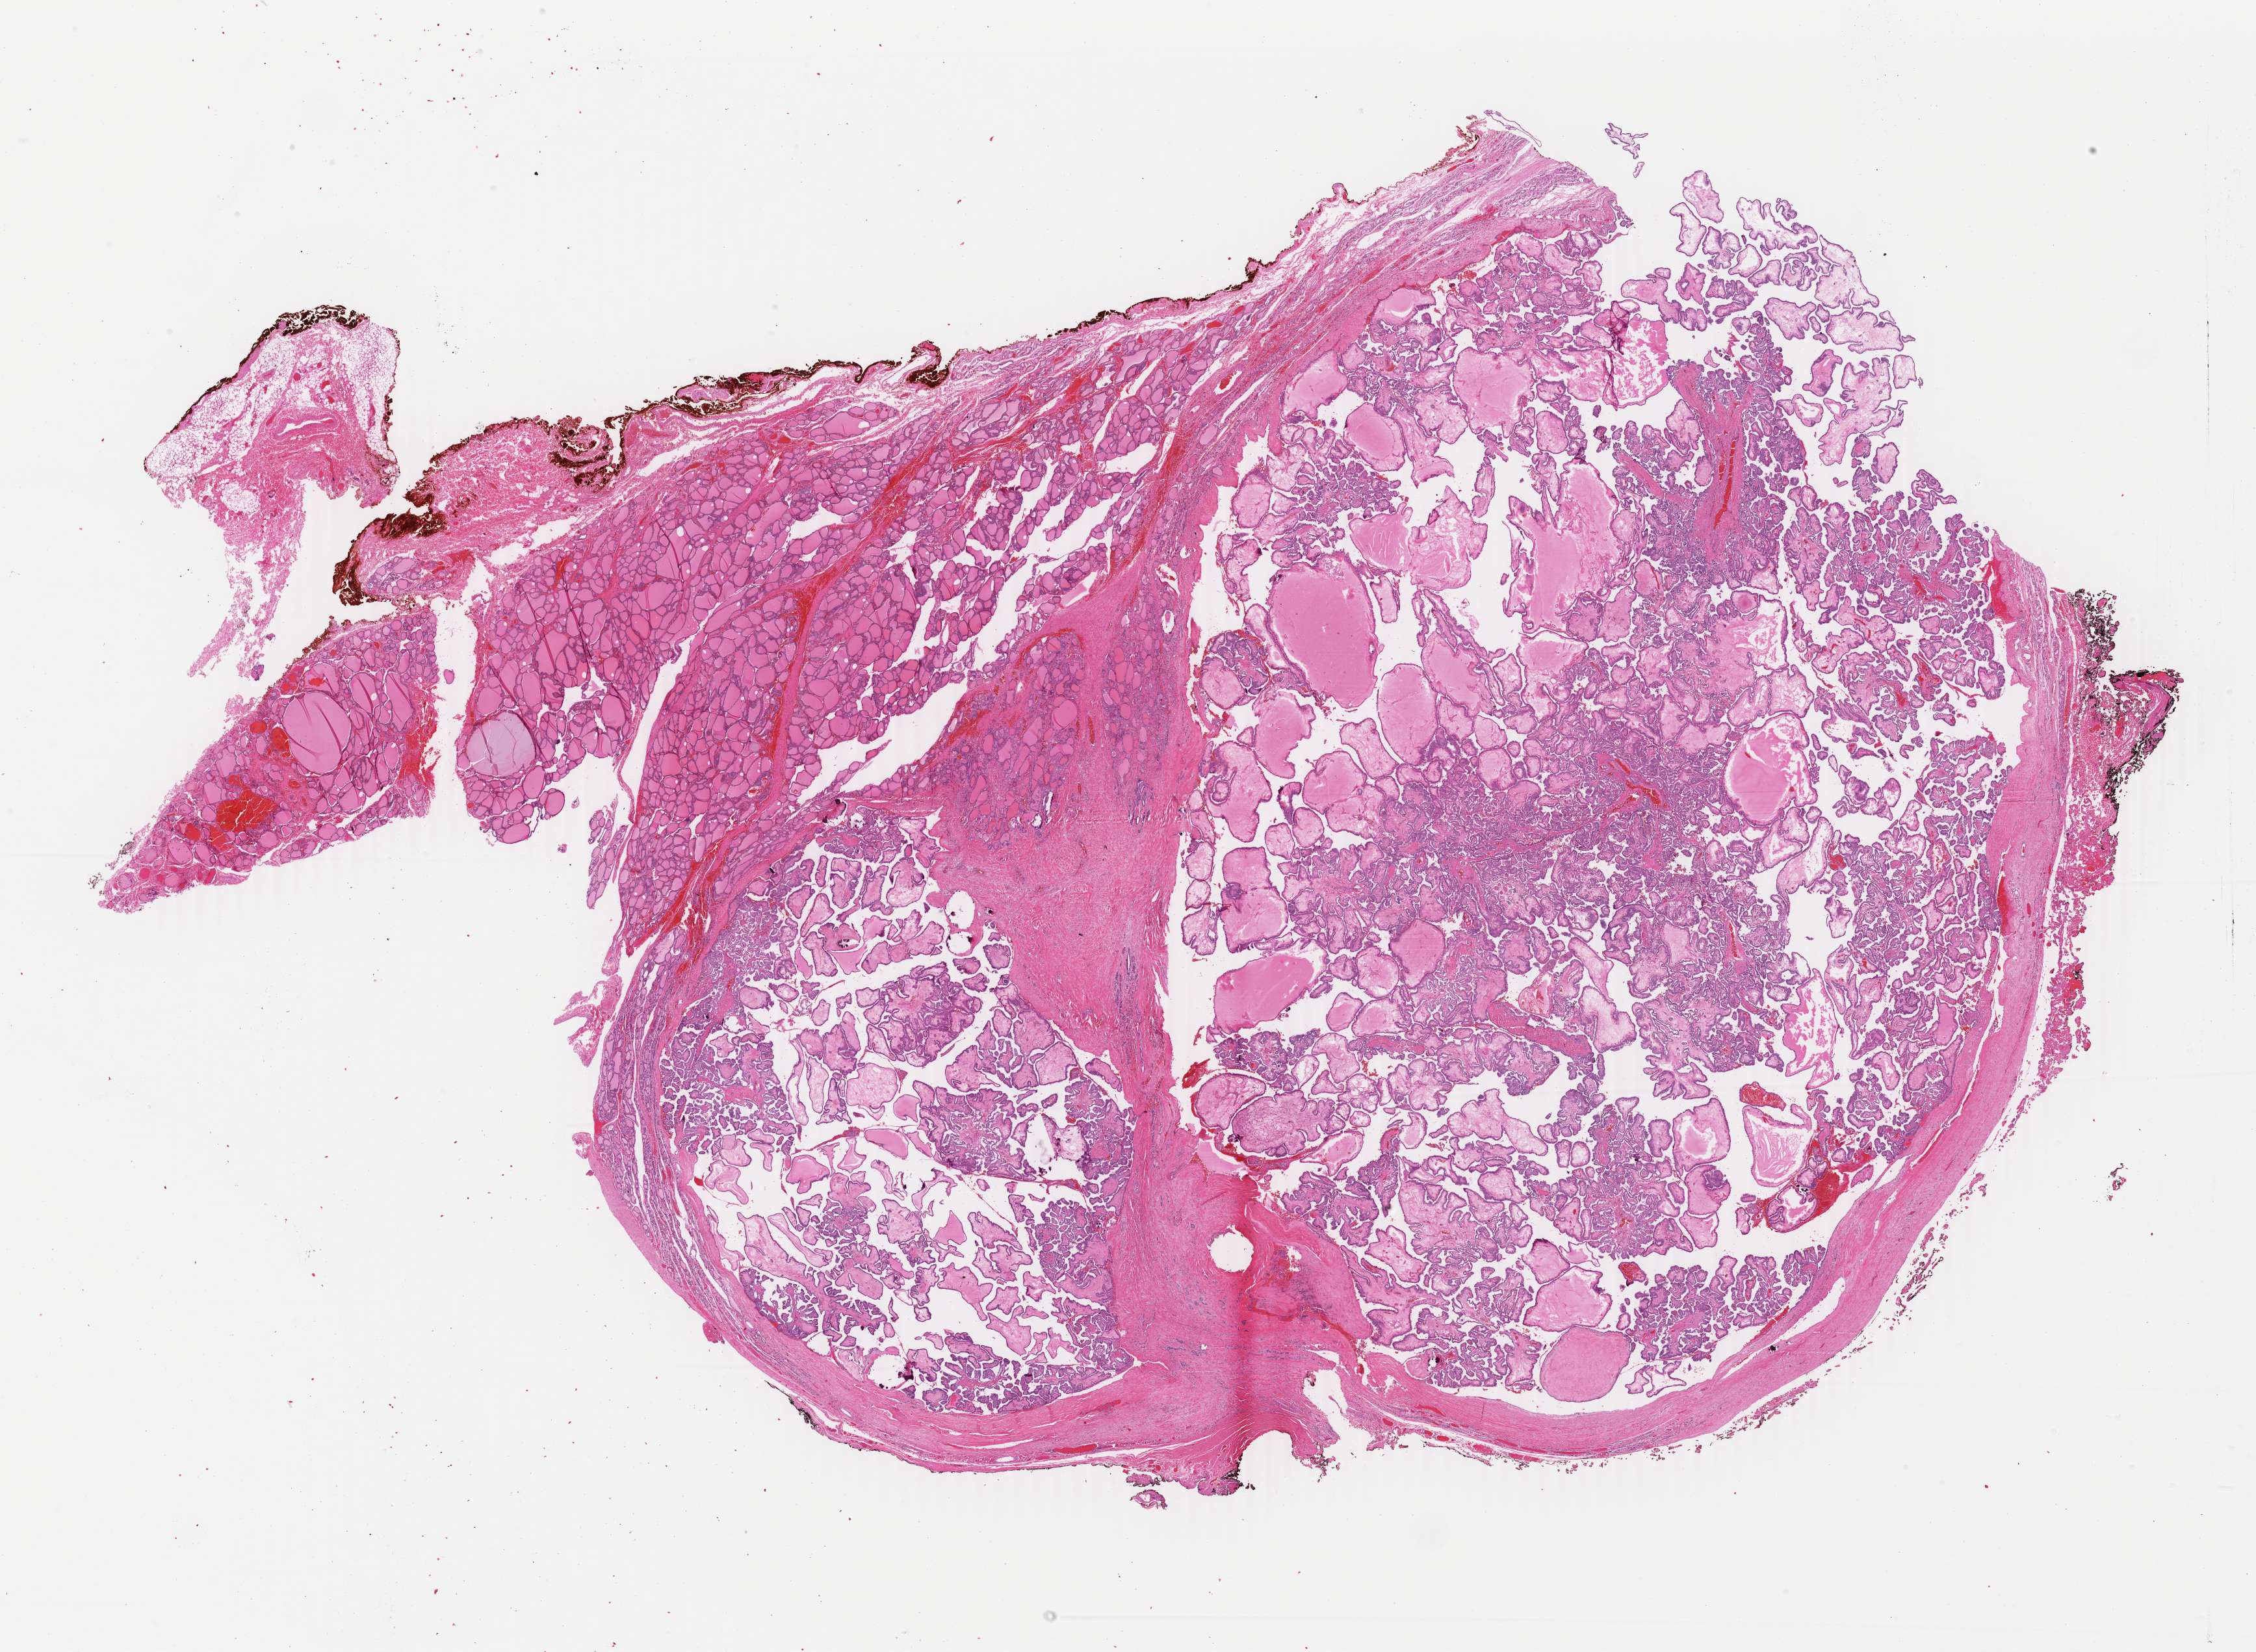
H&E whole-slide image, whole scanned area (about 27.6 x 20.2 mm, slide scanned at 40x) shown as a low-resolution overview. Formalin-fixed paraffin-embedded (FFPE) diagnostic section. Sample: primary tumour, thyroid. Female patient; age at initial diagnosis 28 years.
AJCC pathologic stage: I (6th edition). Pathologic diagnosis: Papillary adenocarcinoma, NOS (thyroid gland).